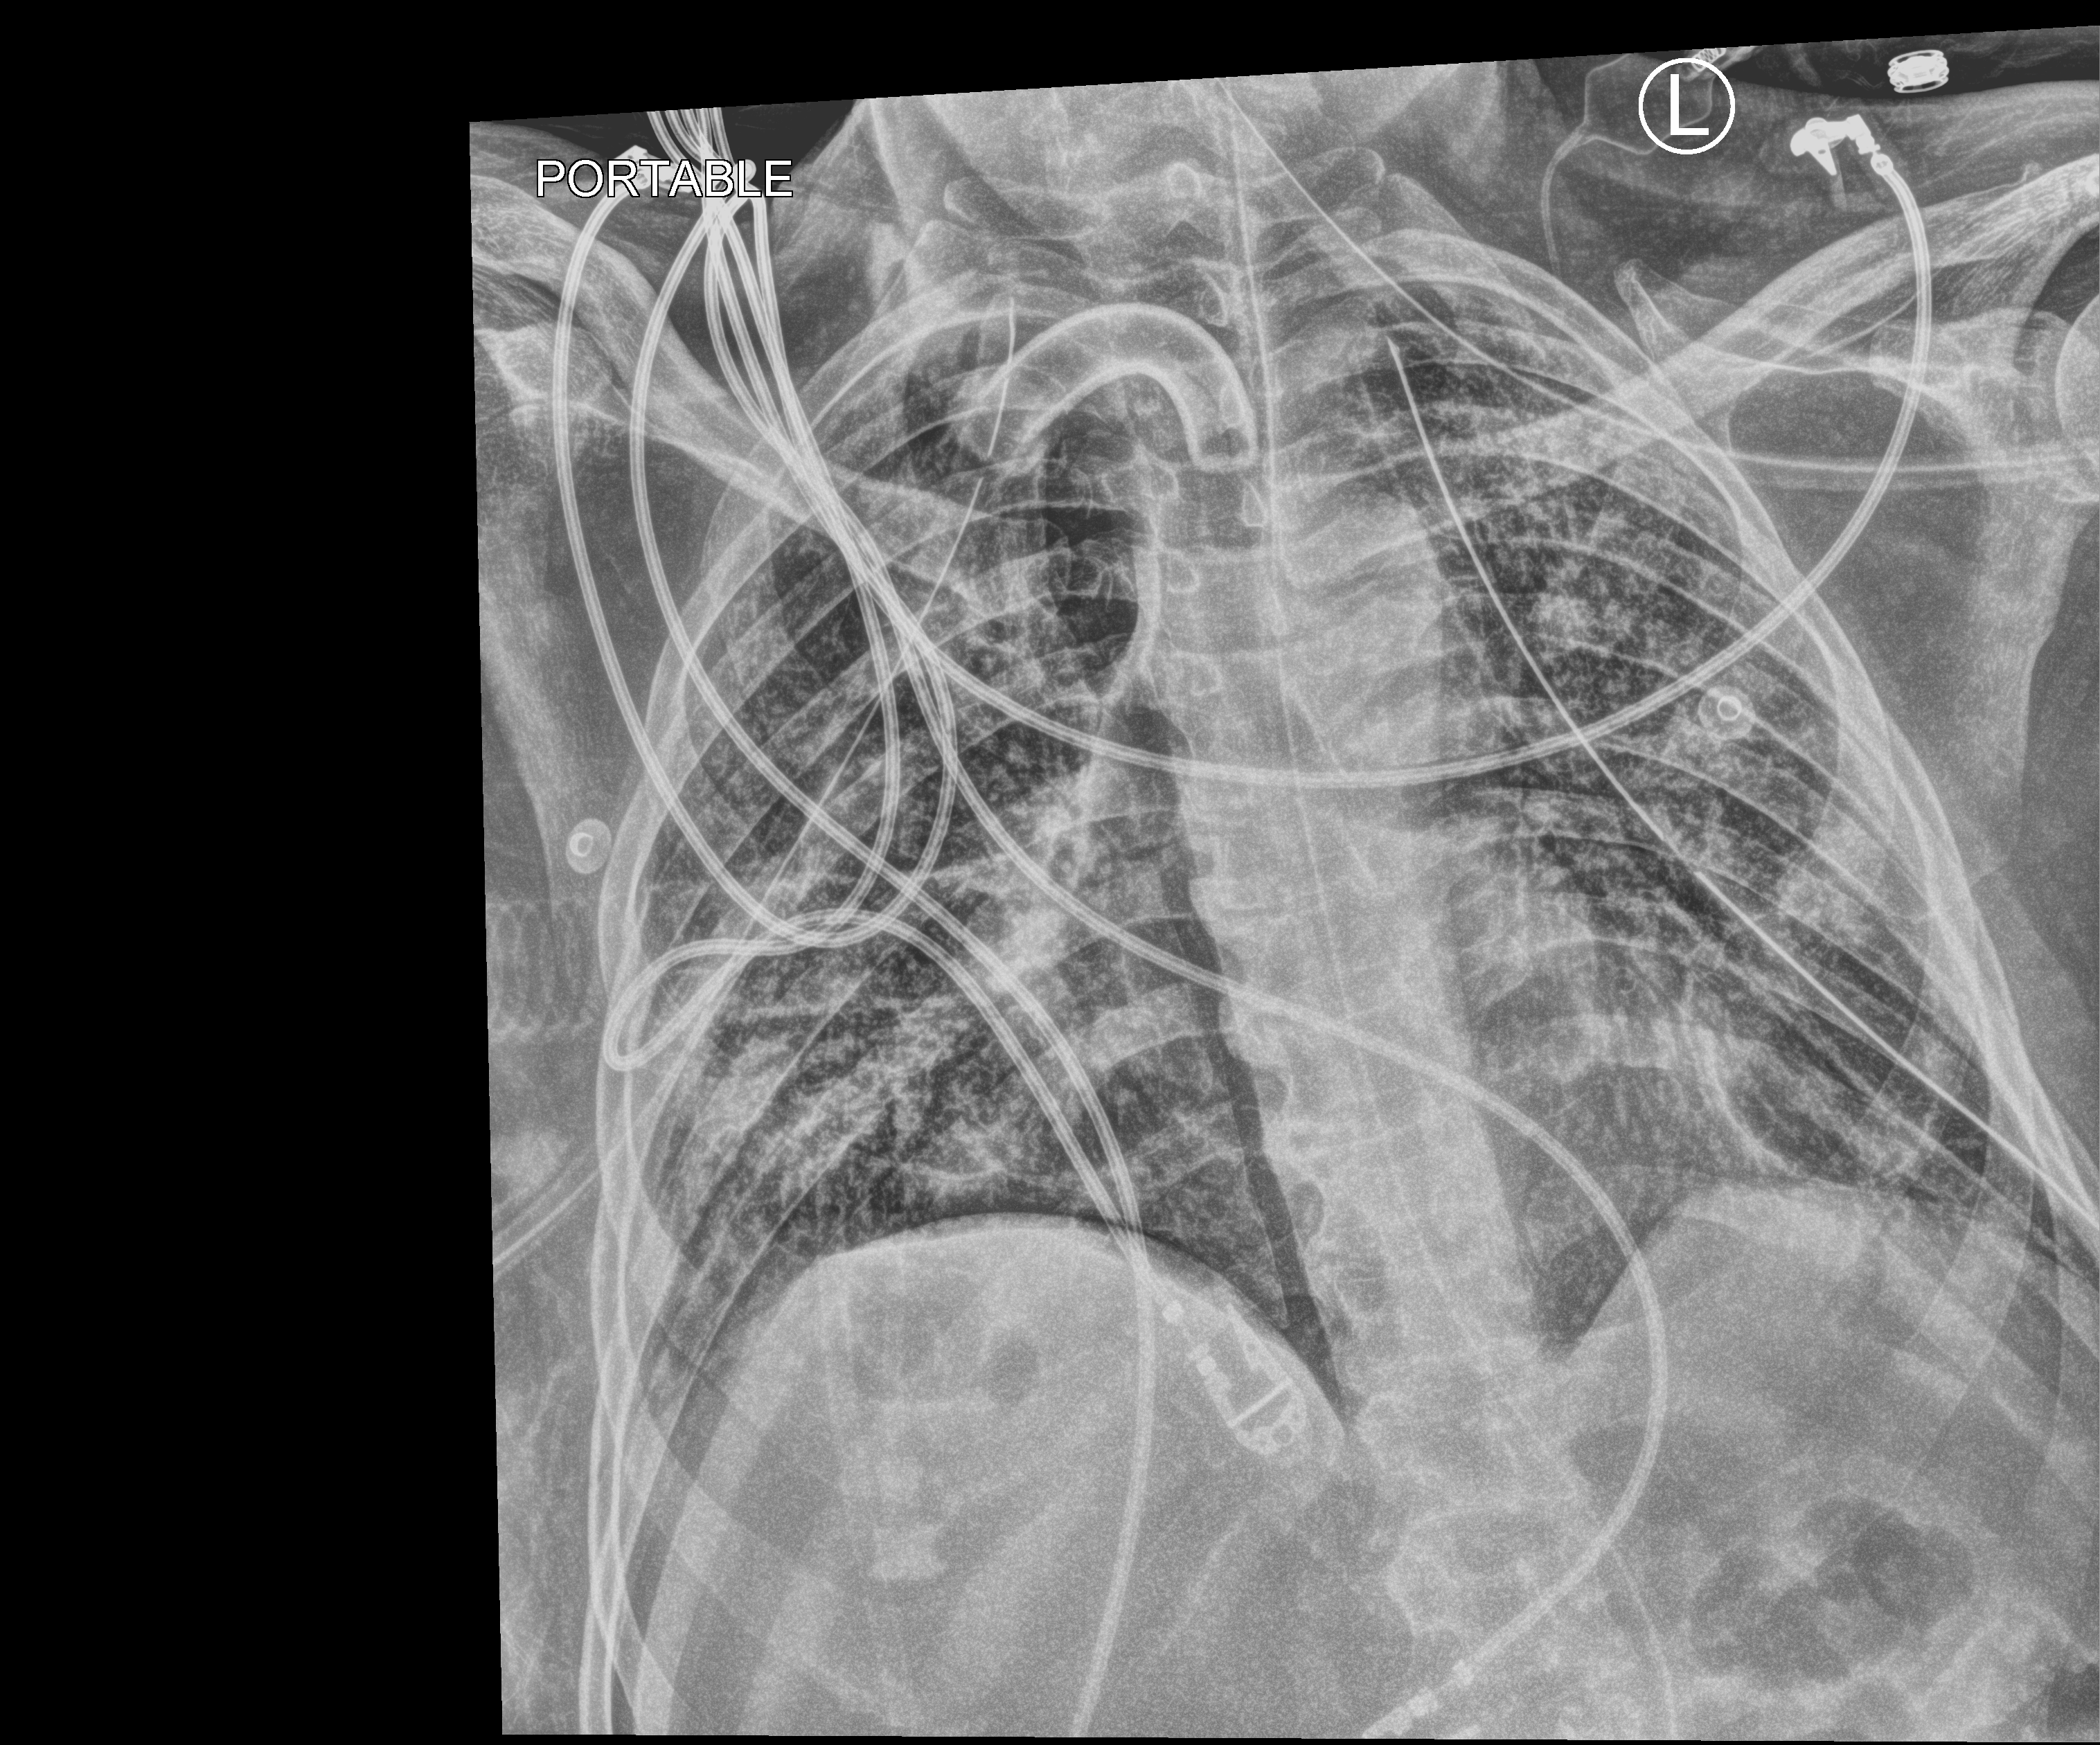
Bedside chest radiograph (computed radiography), anteroposterior (AP) projection. Patient hospitalised with COVID-19; male, aged 18–59 years.
Hospital-stay facts (about this admission, not read from this image; timing relative to this image not recorded):
- admitted to intensive care during this hospital stay: yes
- COPD (admission record): no
- length of hospital stay: 83 days